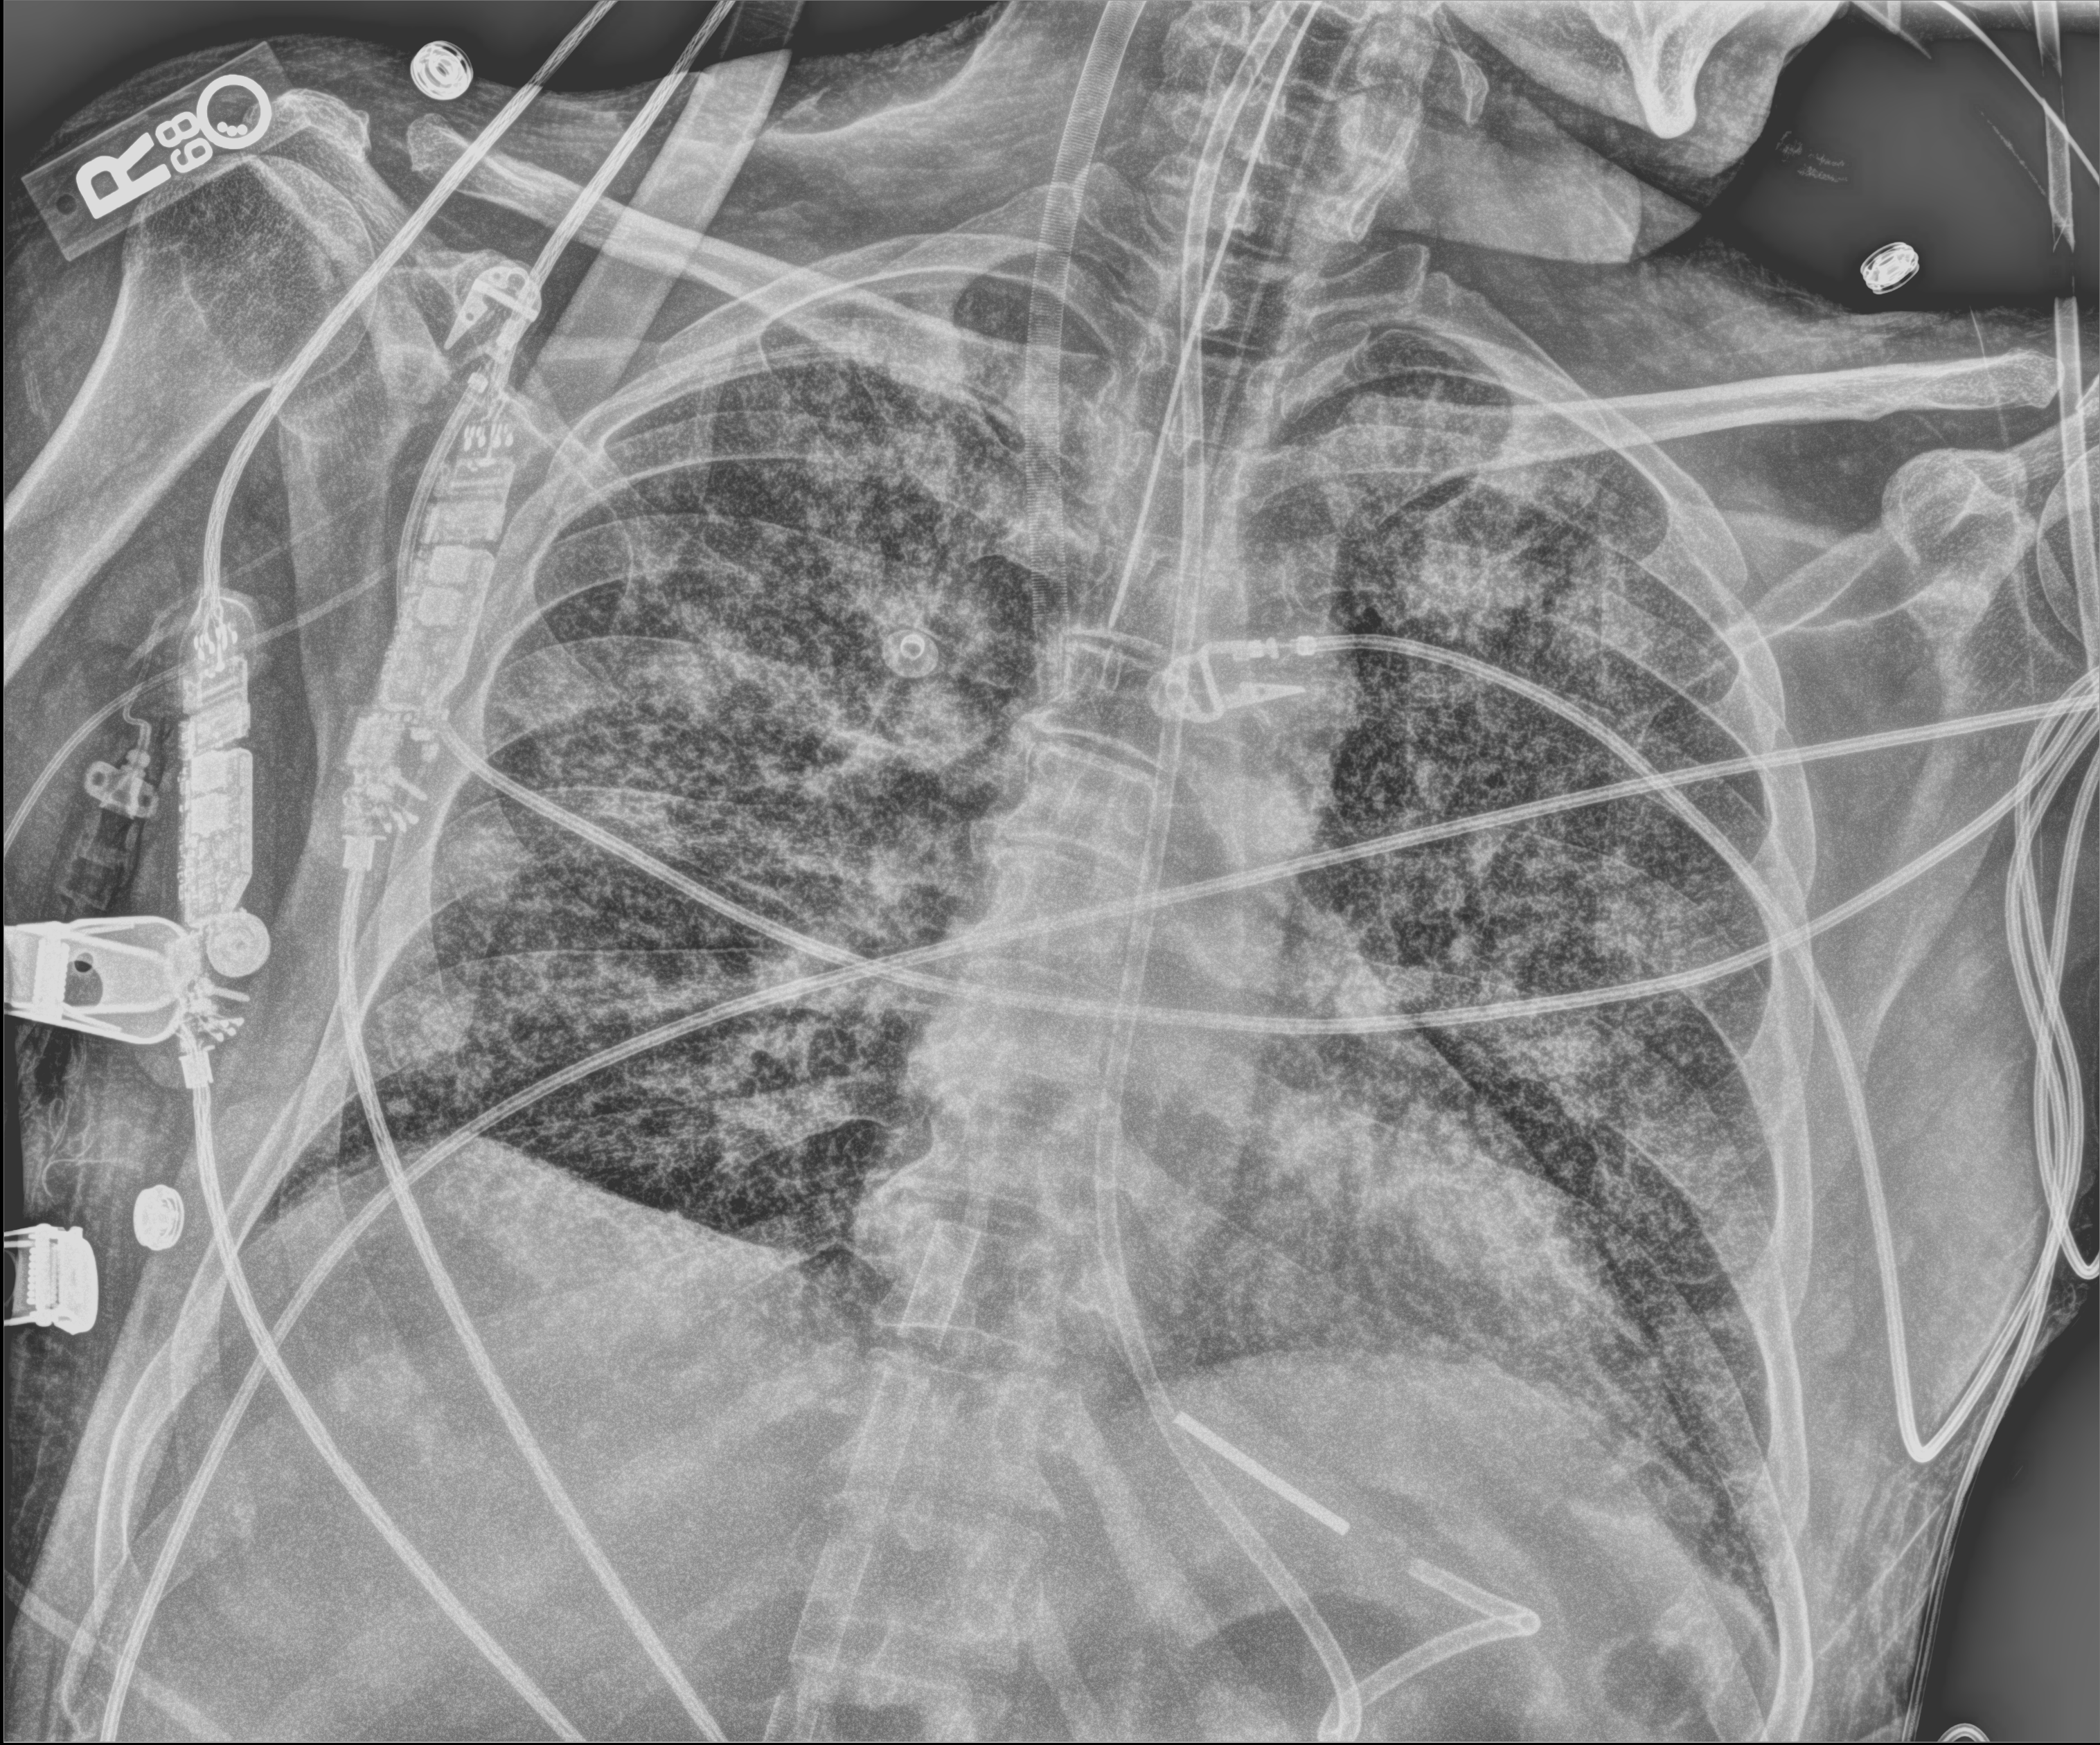
Chest radiograph, anteroposterior (AP) projection. Patient hospitalised with COVID-19; male, aged 18–59 years.
From the hospital-stay record, not from the radiograph (when in the stay this image was taken is not recorded): diabetes (admission record): no; admitted to intensive care during this hospital stay: yes.